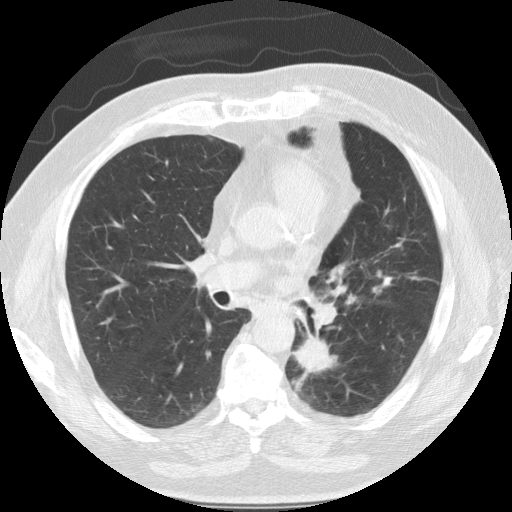
Low-dose screening chest CT, one axial slice; slice 66 of 124 in the series (ordered by position); reconstruction kernel STANDARD; lung window (W 1500 / L -600 HU); 2.5 mm slice thickness; 512 × 512 image matrix.
Structures marked on this image (expert manual segmentation):
- lesion 1 (tumor, lower lobe of left lung): box from (x=290, y=338) to (x=337, y=393) px